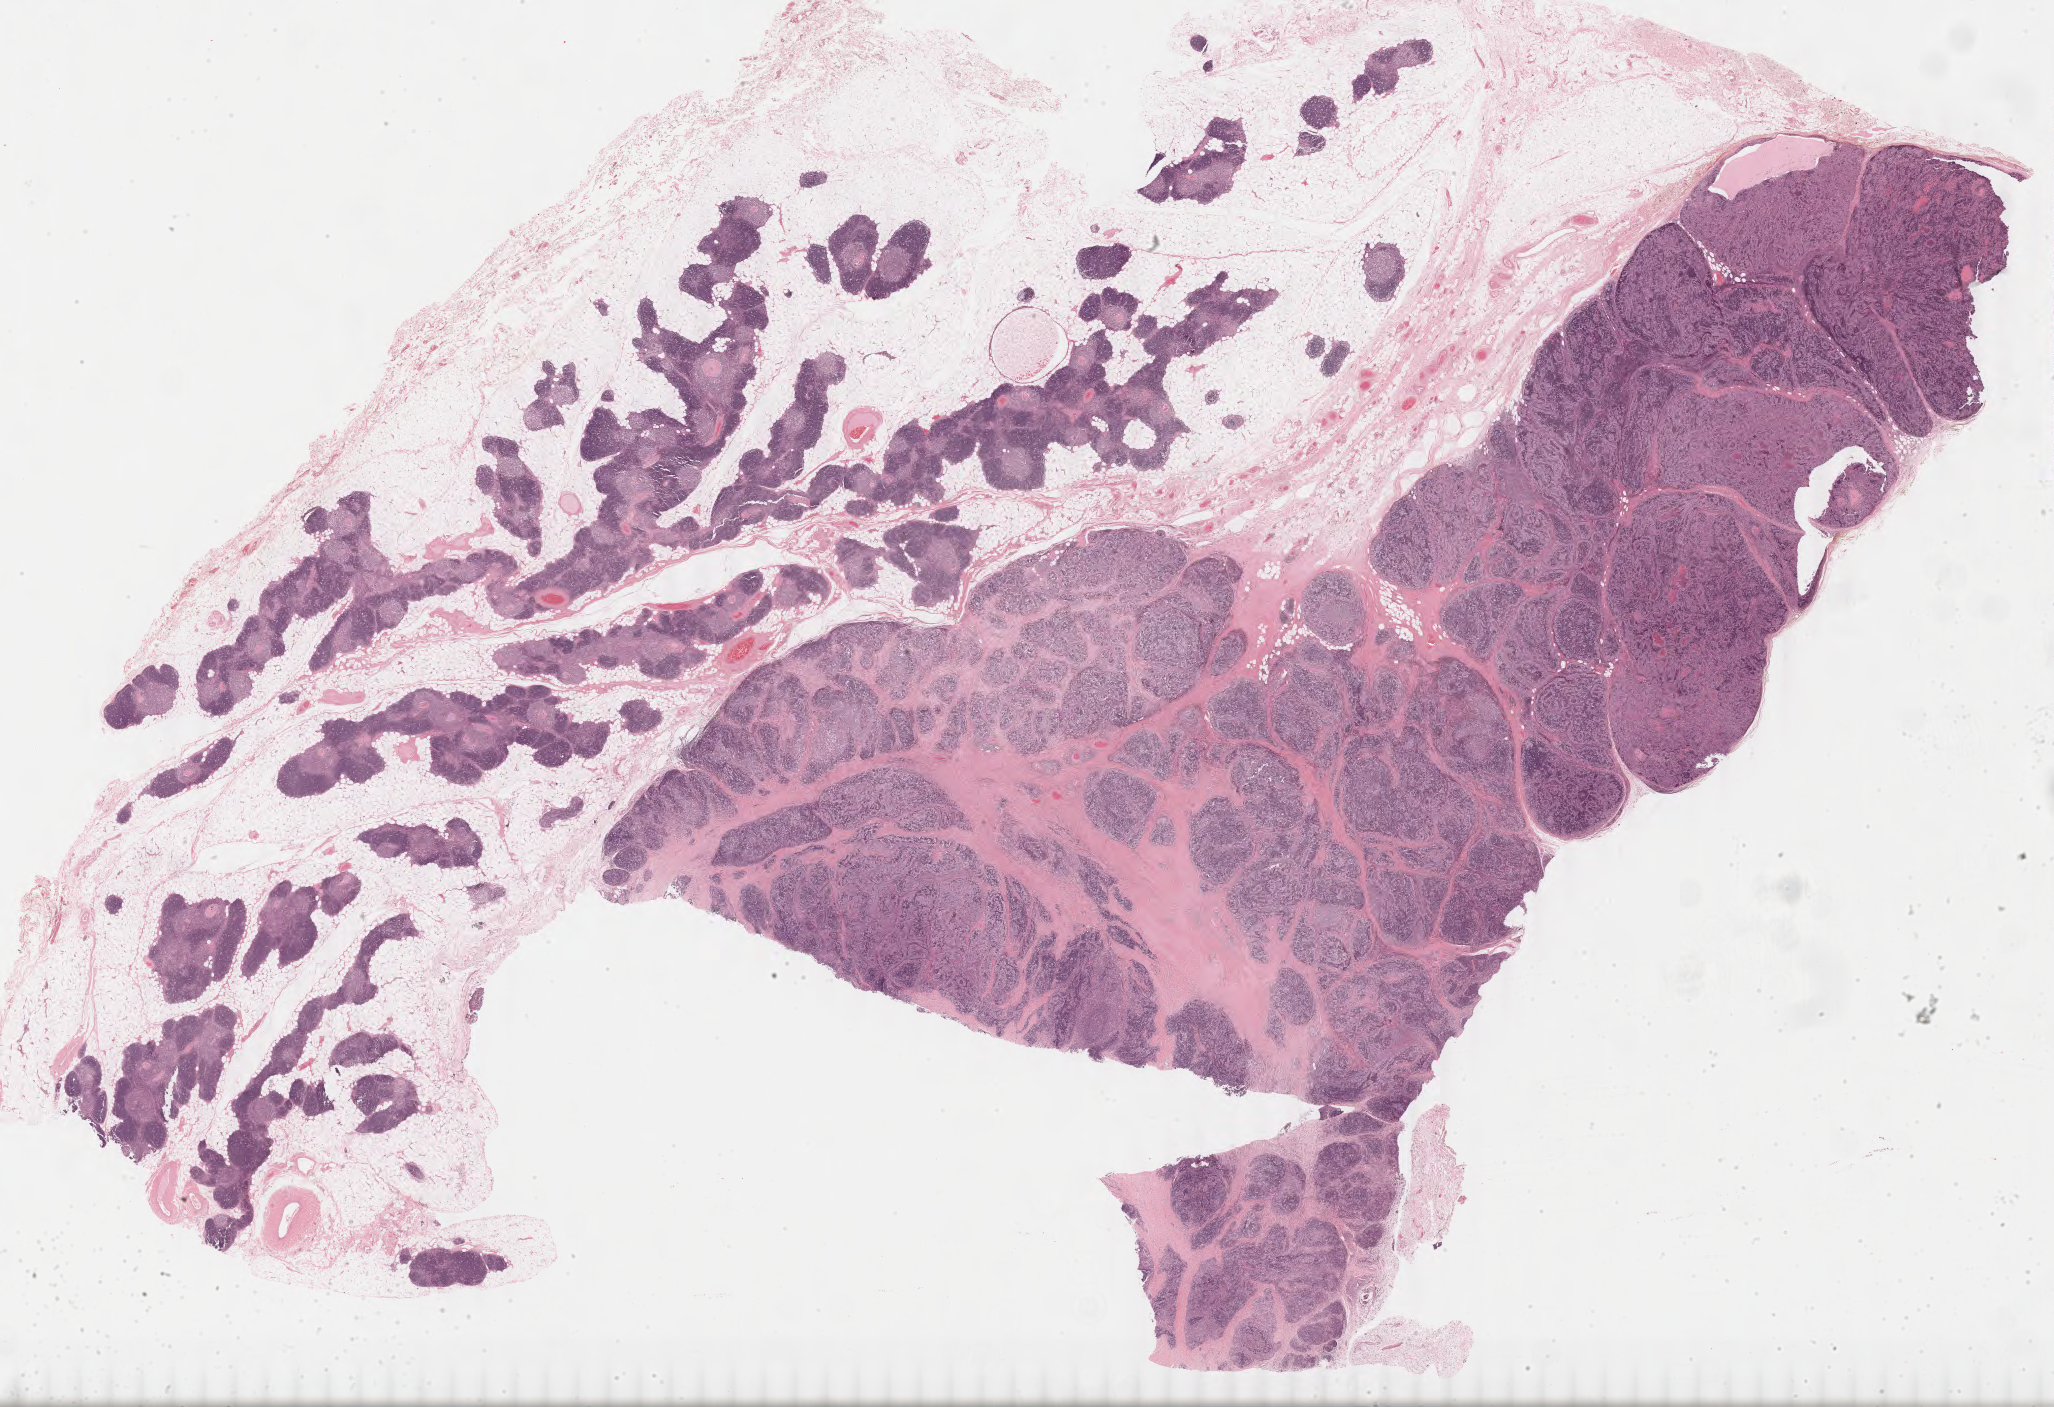
H&E-stained whole-slide image — whole scanned area (about 32.4 x 22.2 mm, acquisition: 40x scan) shown as a low-resolution overview; formalin-fixed paraffin-embedded (FFPE) diagnostic section; sample: primary tumour, thymus. Female, age 39 years at initial diagnosis.
• histologic diagnosis: Thymoma, type B2, malignant